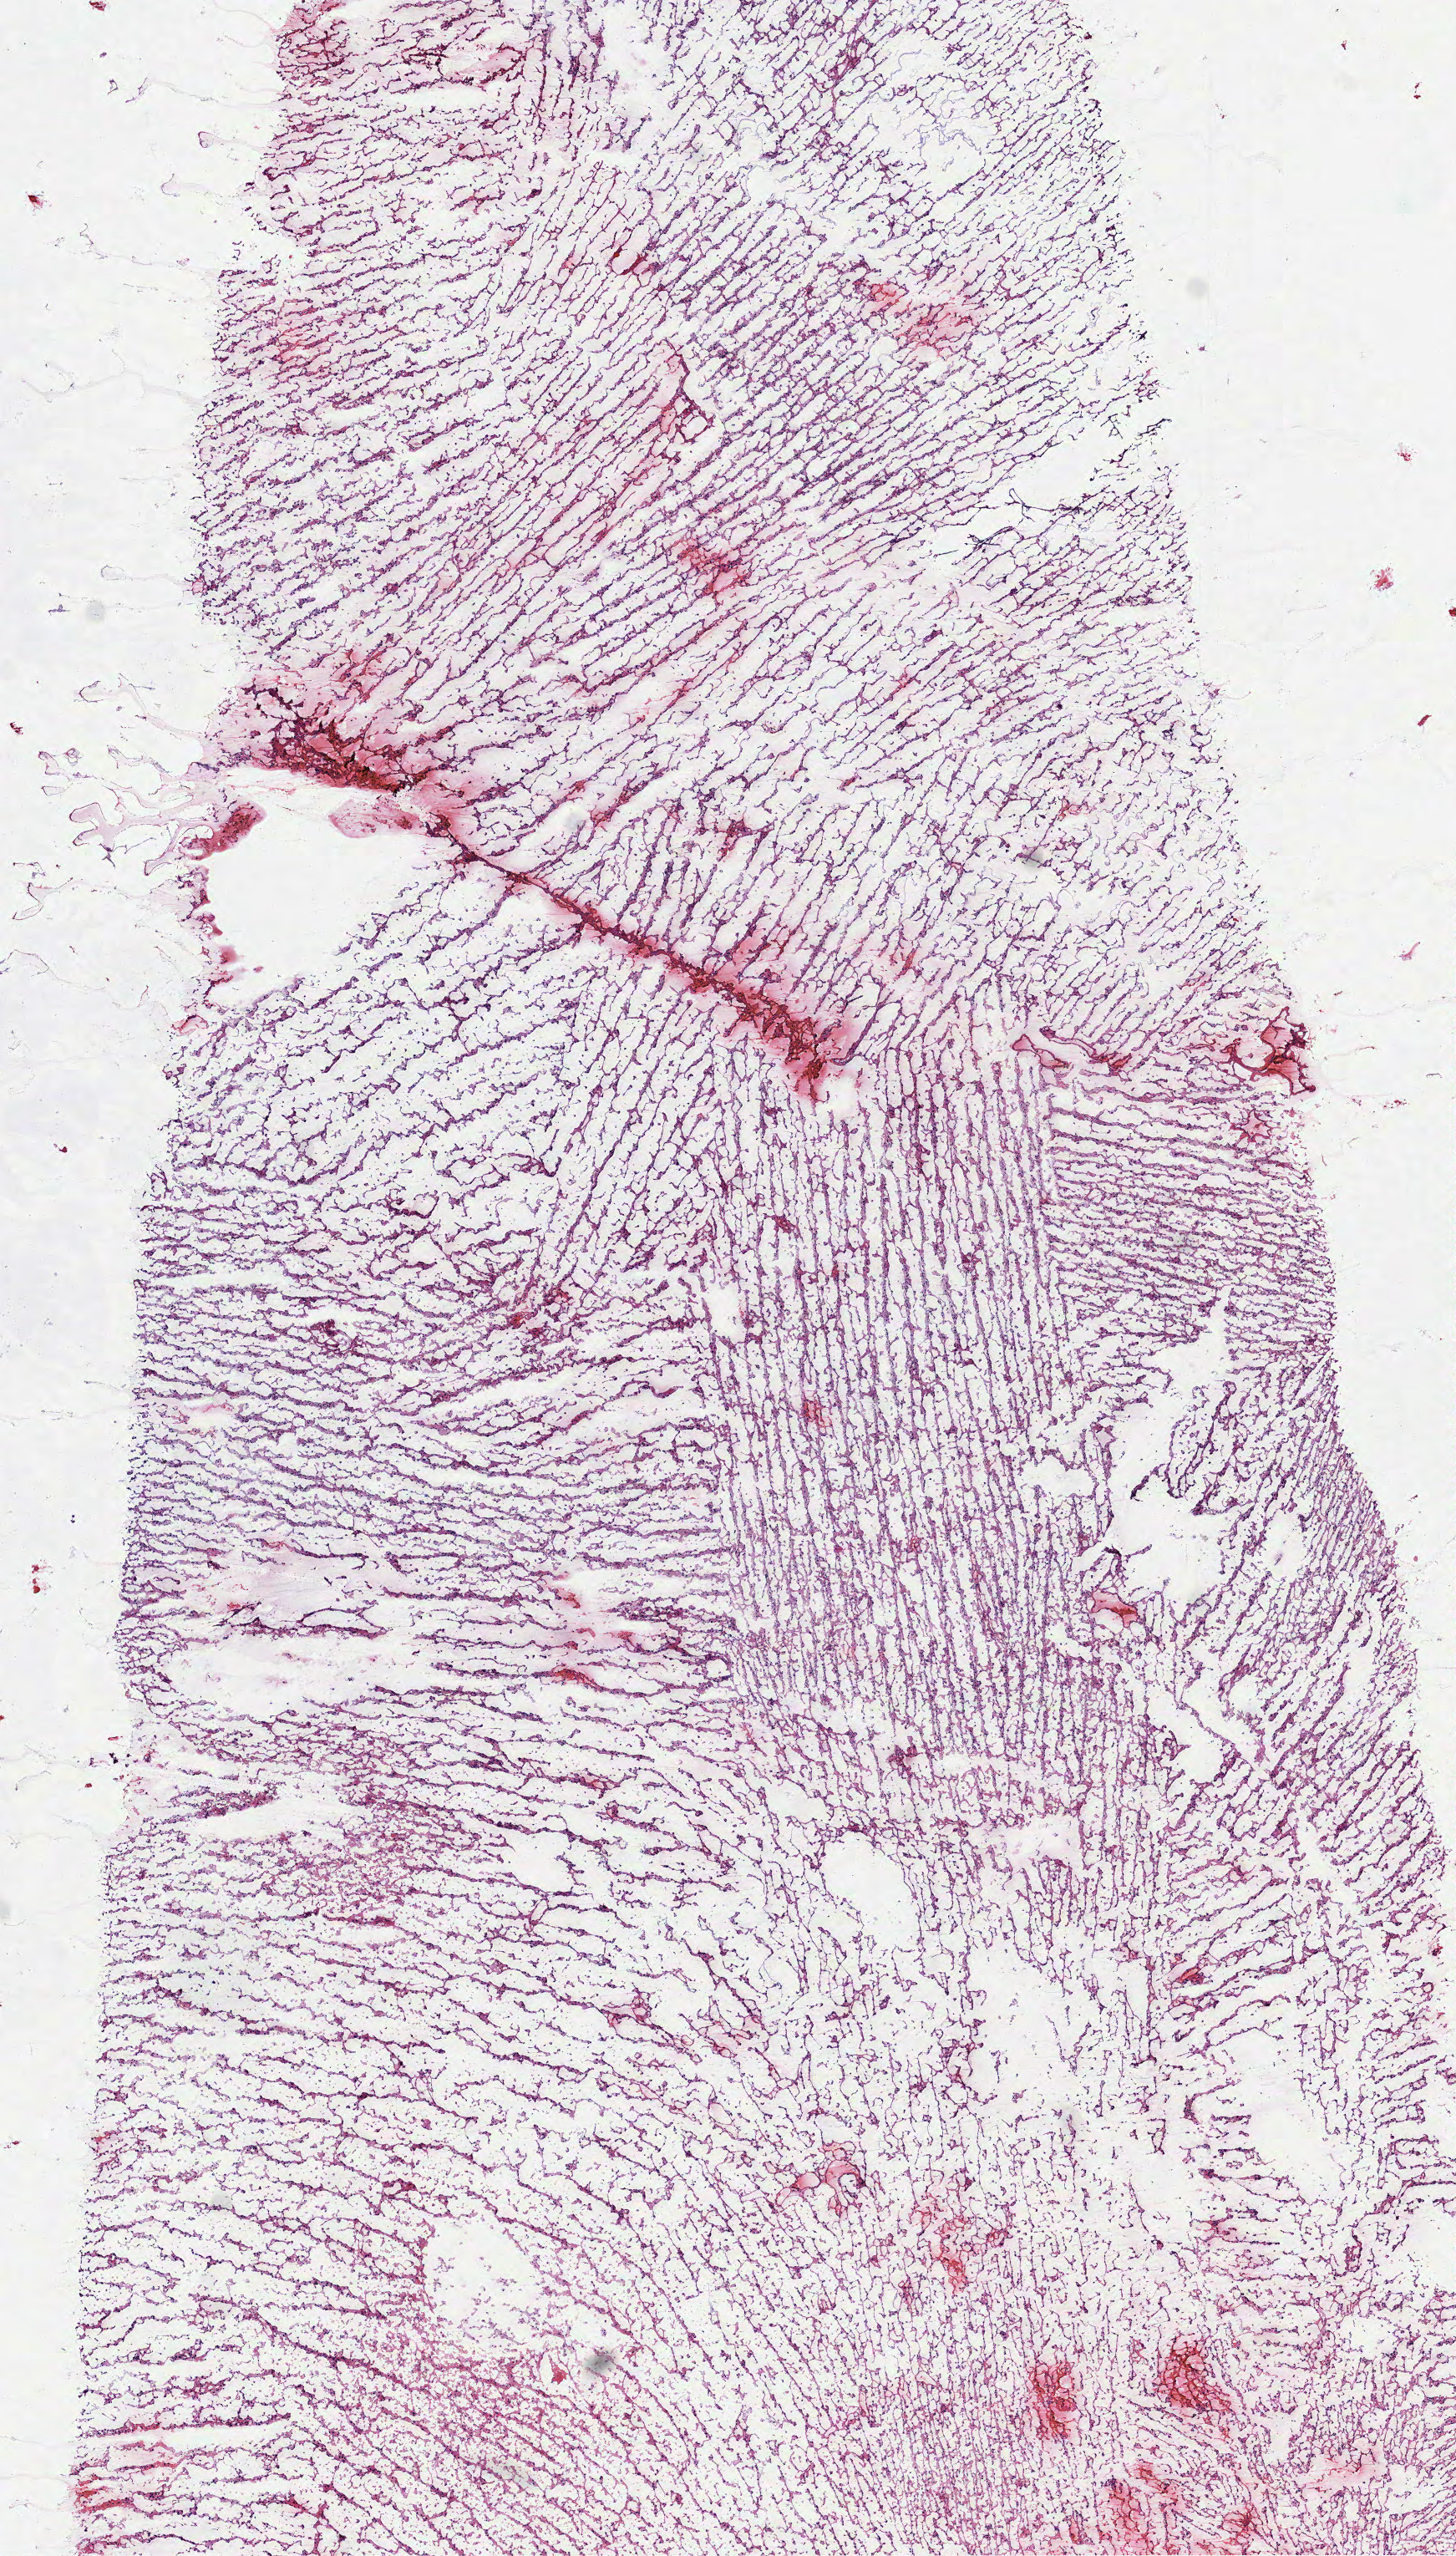
Digitized H&E-stained tissue section (whole slide), shown as a low-resolution overview of the whole scanned area (about 7.0 x 12.3 mm). Frozen section from the top of the tissue portion. Primary tumour sample from the brain. Male patient; age at initial diagnosis 22 years. Slide review estimates, as recorded: tumour cells 100%, tumour nuclei 75%.
Diagnosis: Astrocytoma, anaplastic.